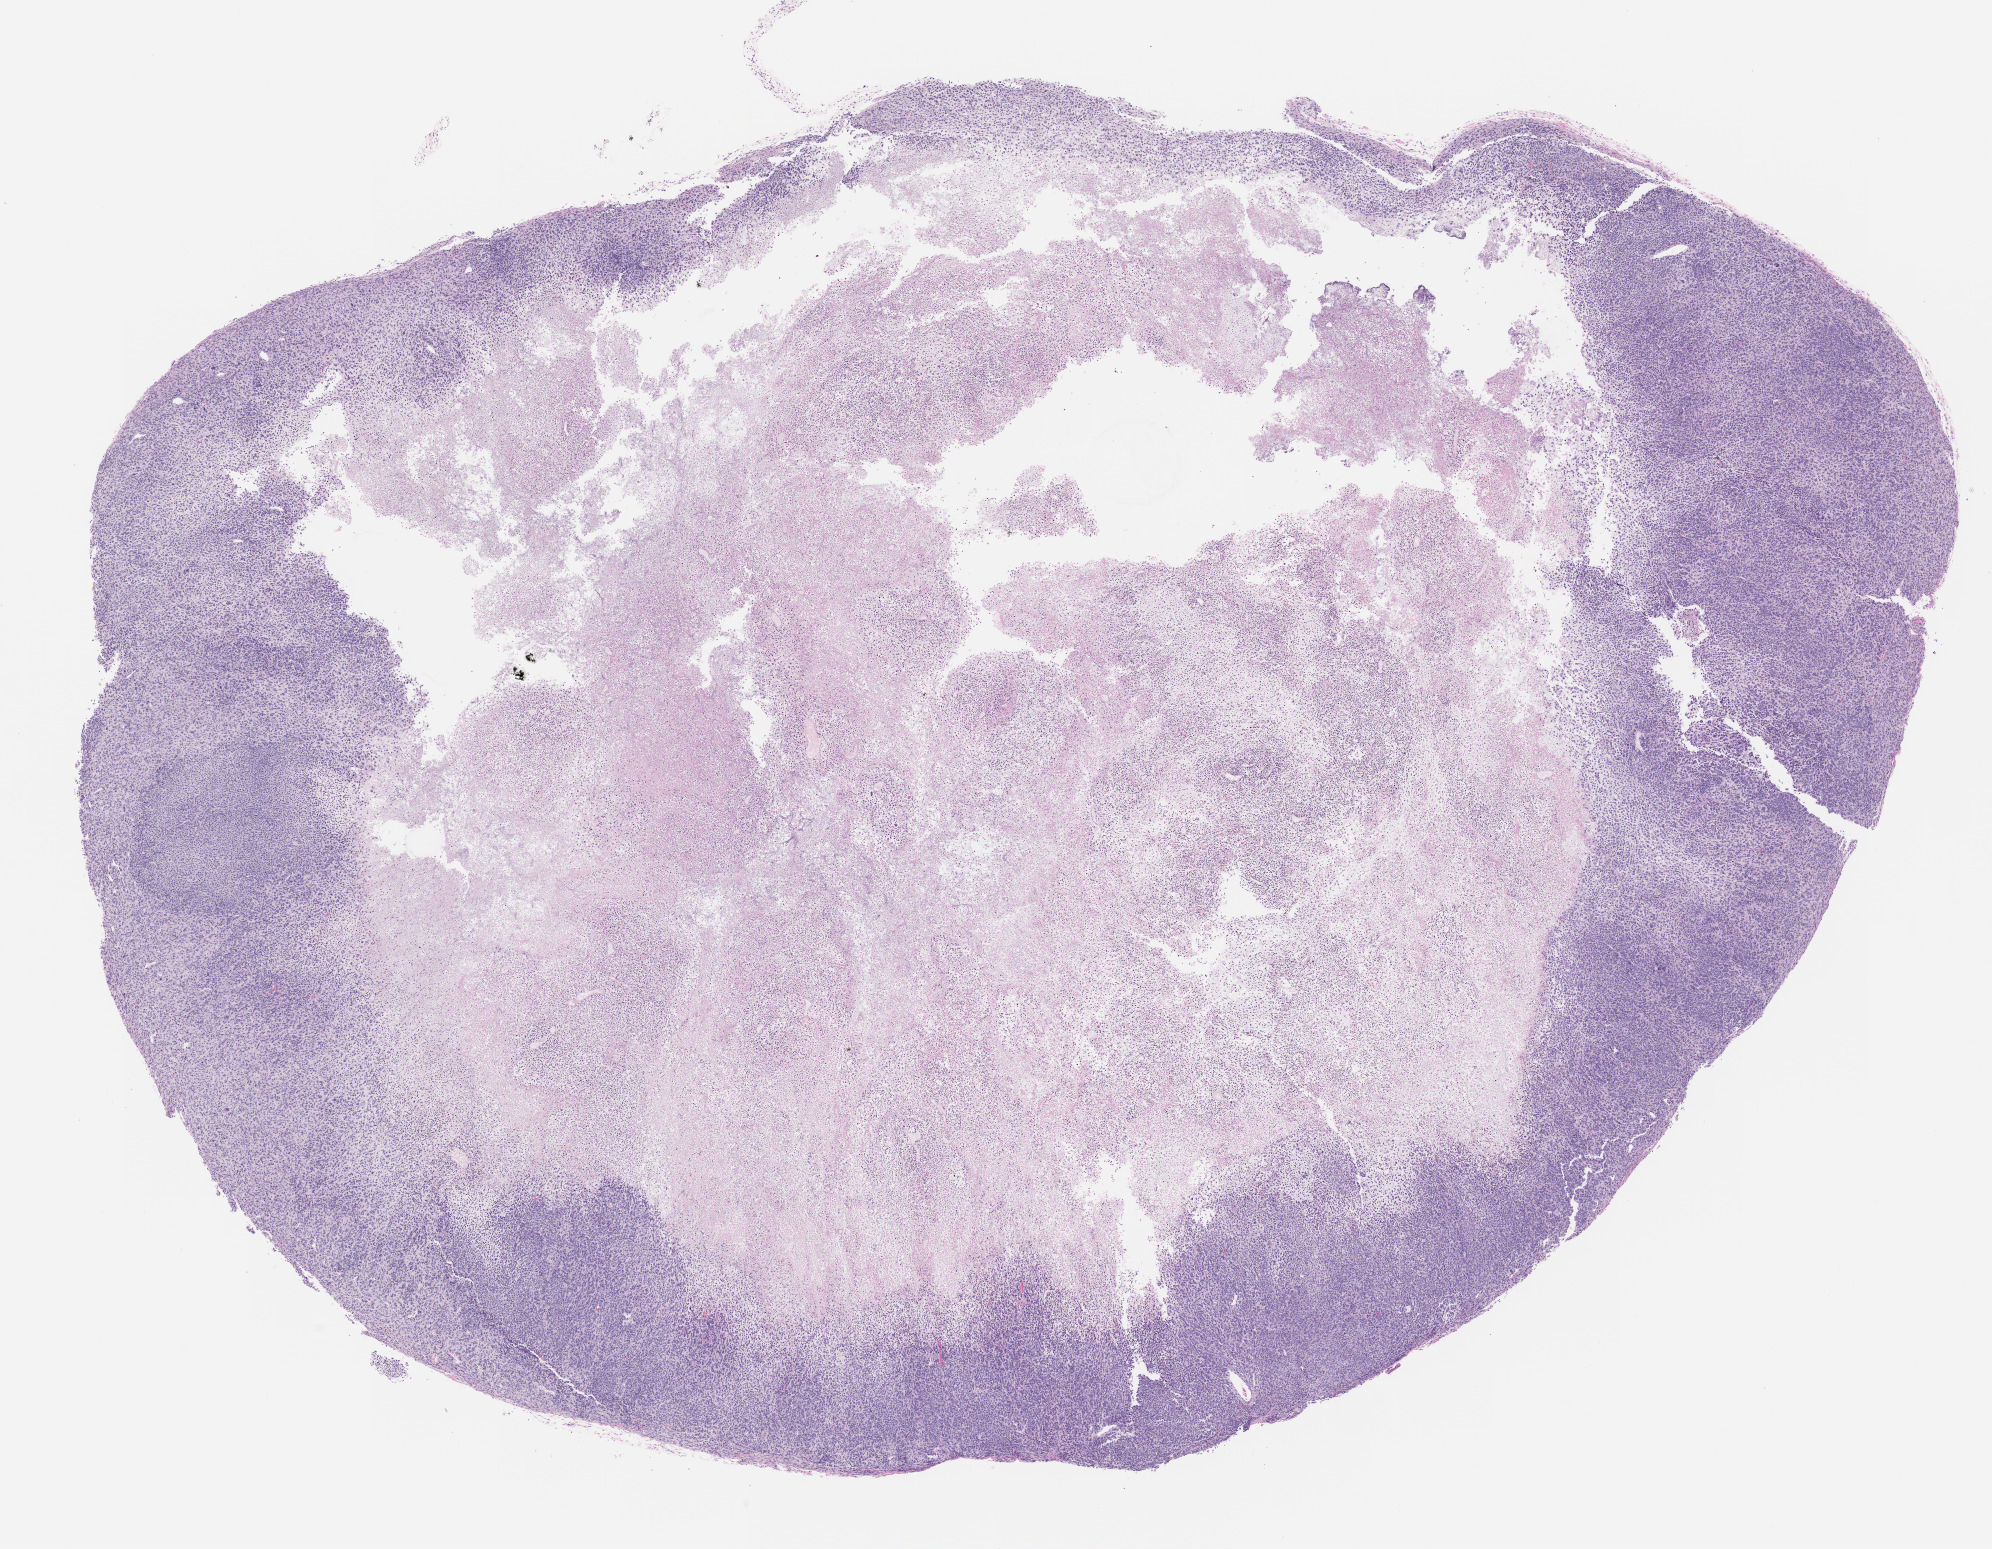
Haematoxylin and eosin whole-slide image of a patient-derived xenograft (PDX) tumor grown in a mouse, passage 1 — shown as a low-resolution overview of the whole scanned area (about 16.0 x 12.5 mm), formalin-fixed paraffin-embedded section, tumor site category: bladder.
Originating patient diagnosis: Urothelial Carcinoma.